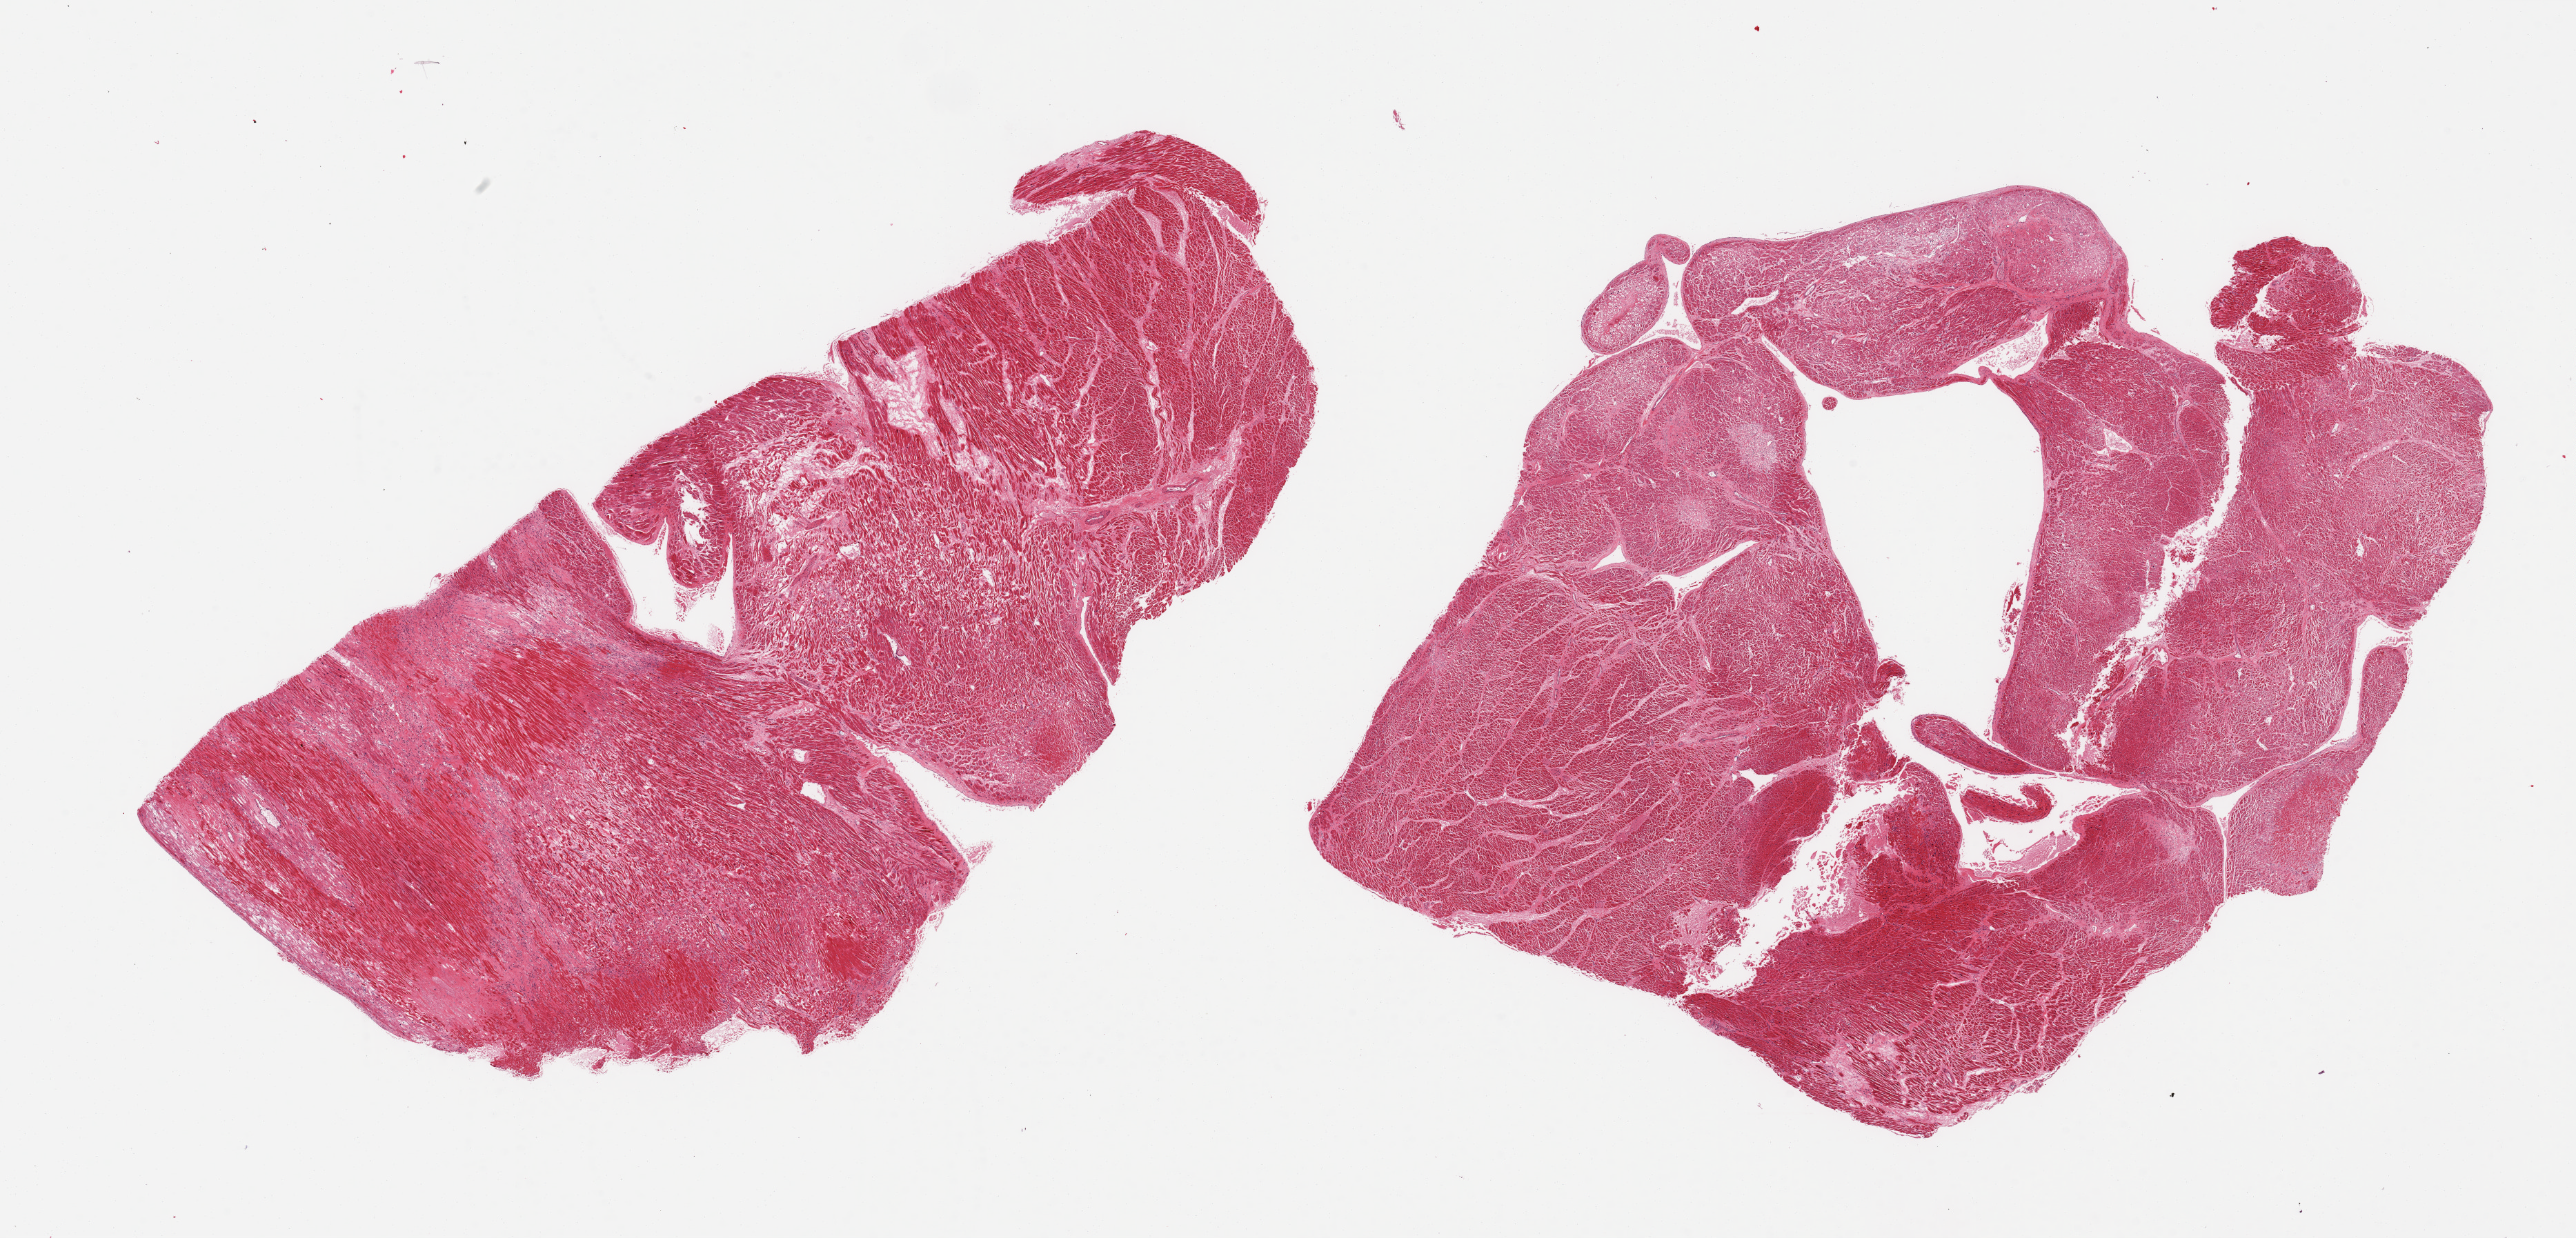
Digitized haematoxylin and eosin-stained section, whole scanned area (about 29.5 x 14.2 mm, slide scanned at 20x) shown as a low-resolution overview, PAXgene-fixed paraffin-embedded (PFPE) section, sampled site (target tissue): heart, tissue donor sample.
* review note (as recorded): 2 pieces; extensive interstitial fibrosis and myofiber vacuolation